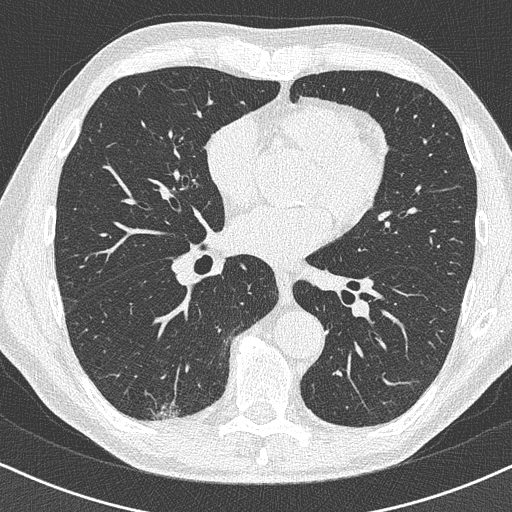
Low-dose screening chest CT, axial slice; first (baseline) screen; lung window (W 1500 / L -600 HU); 120 kVp. Male participant, aged 63 years at enrolment. Former smoker at enrolment.
Expert-annotated lung lesion, box from (x=125, y=354) to (x=198, y=427) px. Screening reader's record for this exam (one nodule recorded; not confirmed to be the boxed lesion): non-calcified nodule or mass ≥4 mm, right lower lobe, 16 × 13 mm, poorly defined margins. Official screen result: positive, change unspecified: nodule(s) >= 4 mm or enlarging nodule(s), mass(es), or other non-specific abnormalities suspicious for lung cancer.